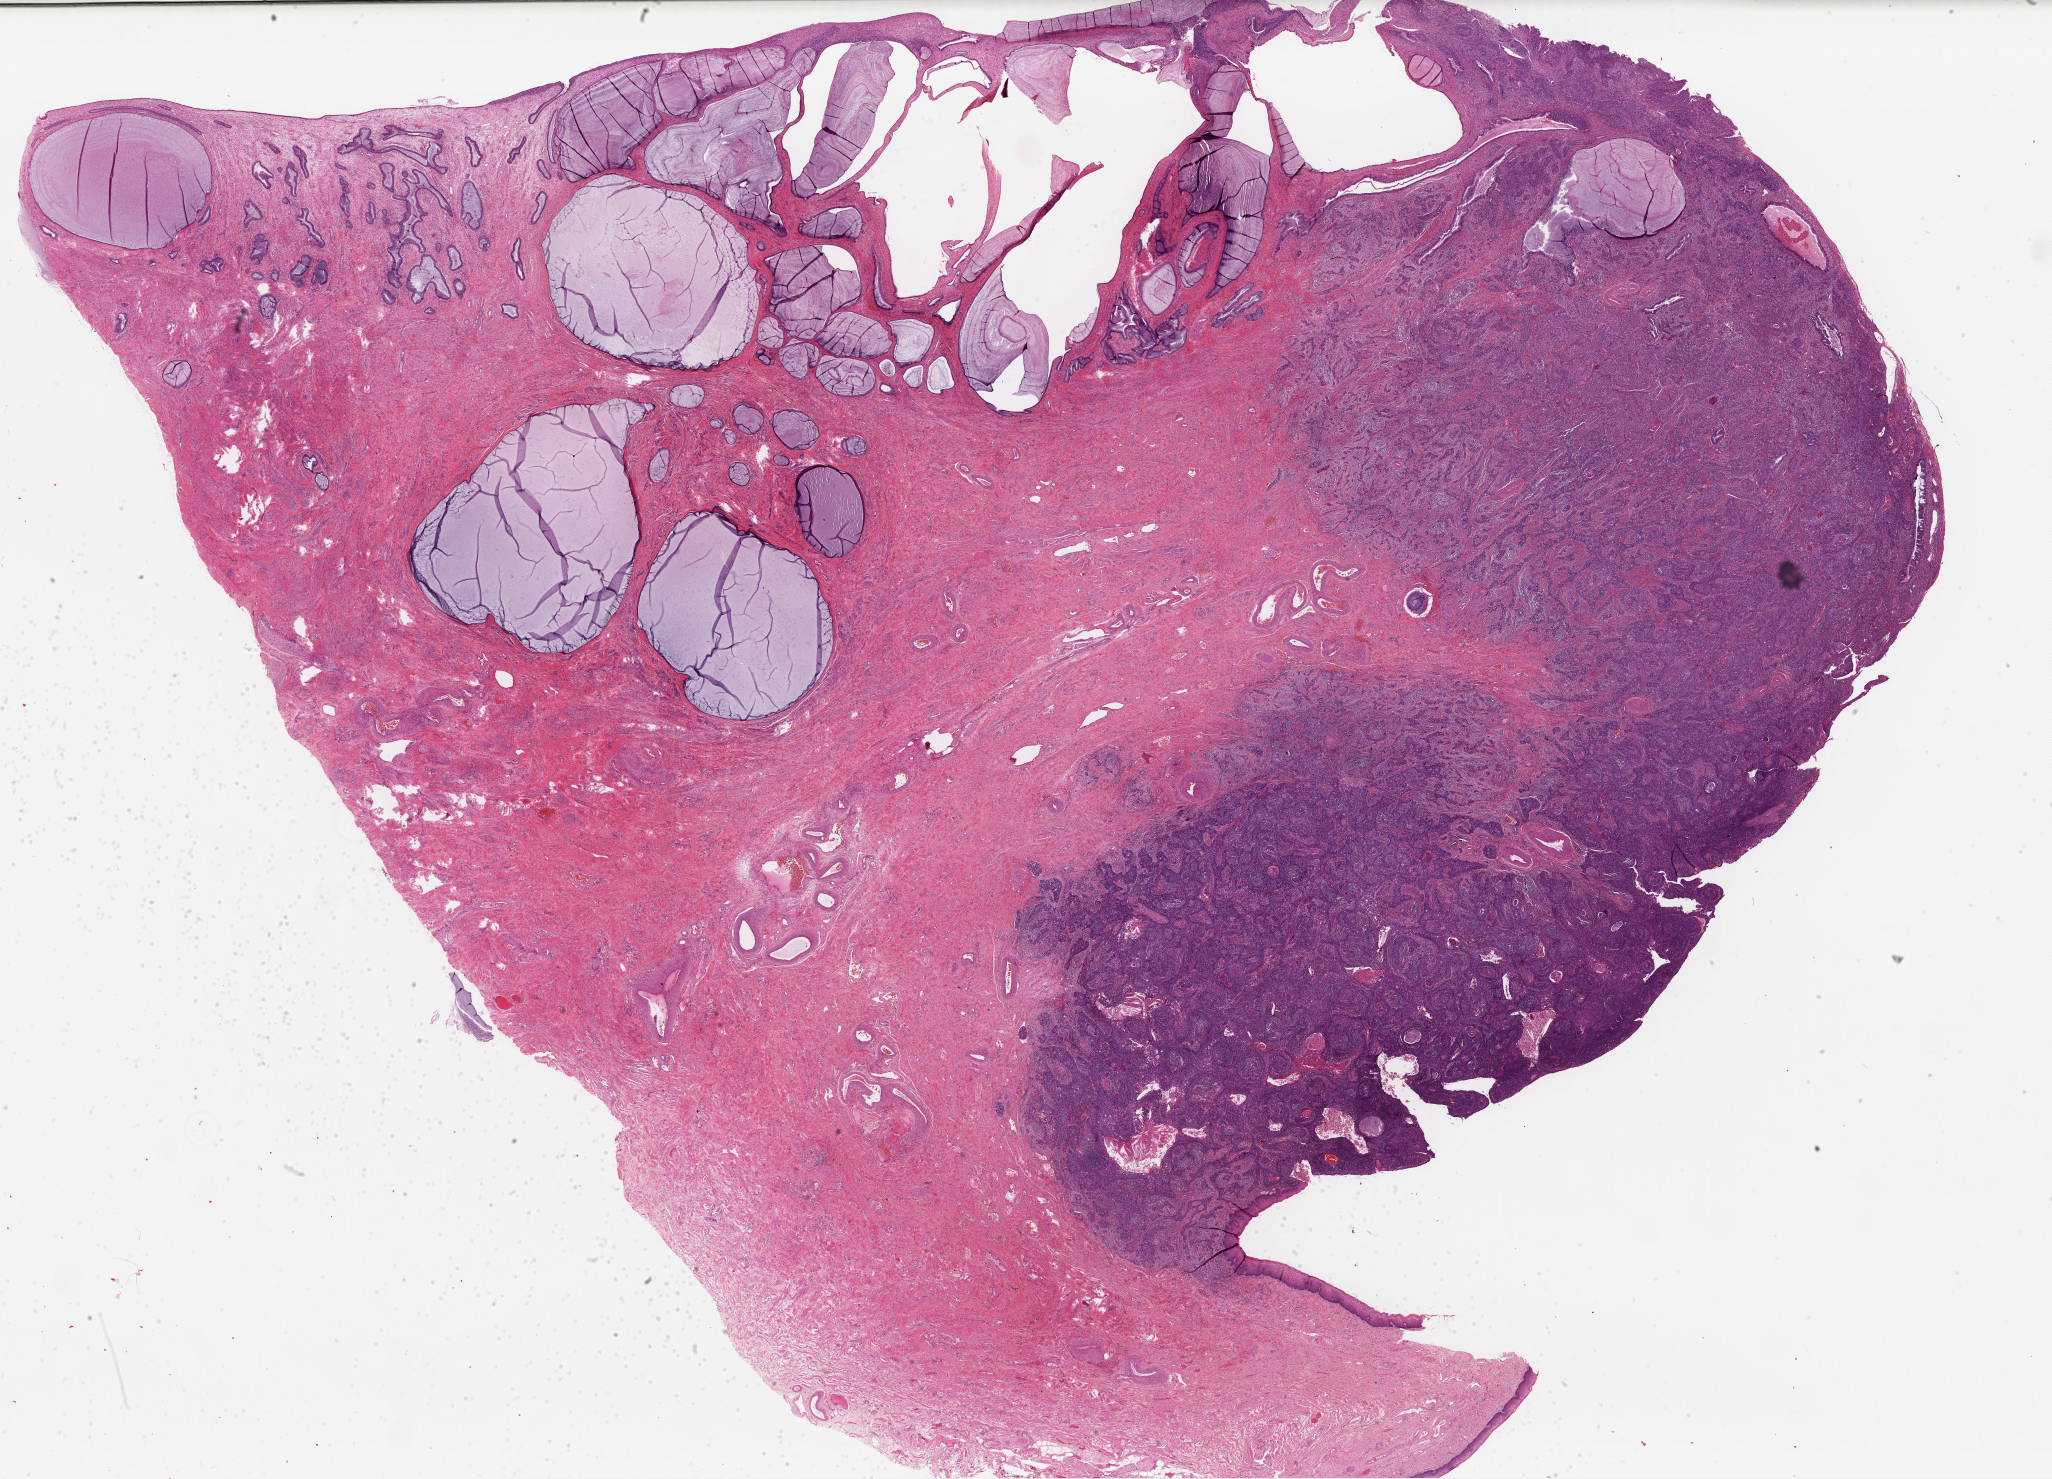
Digitized H&E-stained tissue section (whole slide) — shown as a low-resolution overview of the whole scanned area (about 32.4 x 23.4 mm, slide scanned at 40x). Formalin-fixed paraffin-embedded (FFPE) diagnostic section. Primary tumour sample from the cervix. Patient: female, age at initial diagnosis 49 years. Histologic grade: G3 (poorly differentiated).
* lymph nodes positive (case pathology): 0 of 16 examined
* FIGO stage: IB1
* histologic diagnosis: Squamous cell carcinoma, NOS (cervix uteri)